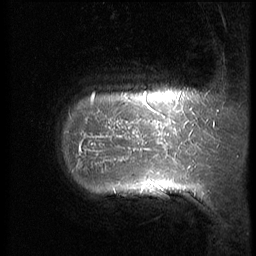
Breast MRI (dynamic contrast-enhanced), one sagittal slice. Slice 9 of 64 in the series (ordered by position). 3 images stored at this slice position (order not interpretable as contrast timing). 1.5 T. TE 4.2 ms, TR 9 ms. 2.5 mm slice thickness. 256 × 256 image matrix. Female patient, age 39 years. From the clinical record (not read from this slice): setting: breast cancer imaged before/during neoadjuvant chemotherapy; receptor status: HER2-positive.
Structures marked on this image (semi-automatic segmentation, software-assisted and operator-edited):
- analysis volume of interest (the breast-tissue region the enhancement analysis was run in; not a lesion): bounding box (x1, y1, x2, y2) in pixels: (51, 60, 210, 239)
- tumour enhancement mask (voxels above the 140 % enhancement threshold inside the analysis volume of interest): (78, 98, 176, 170)